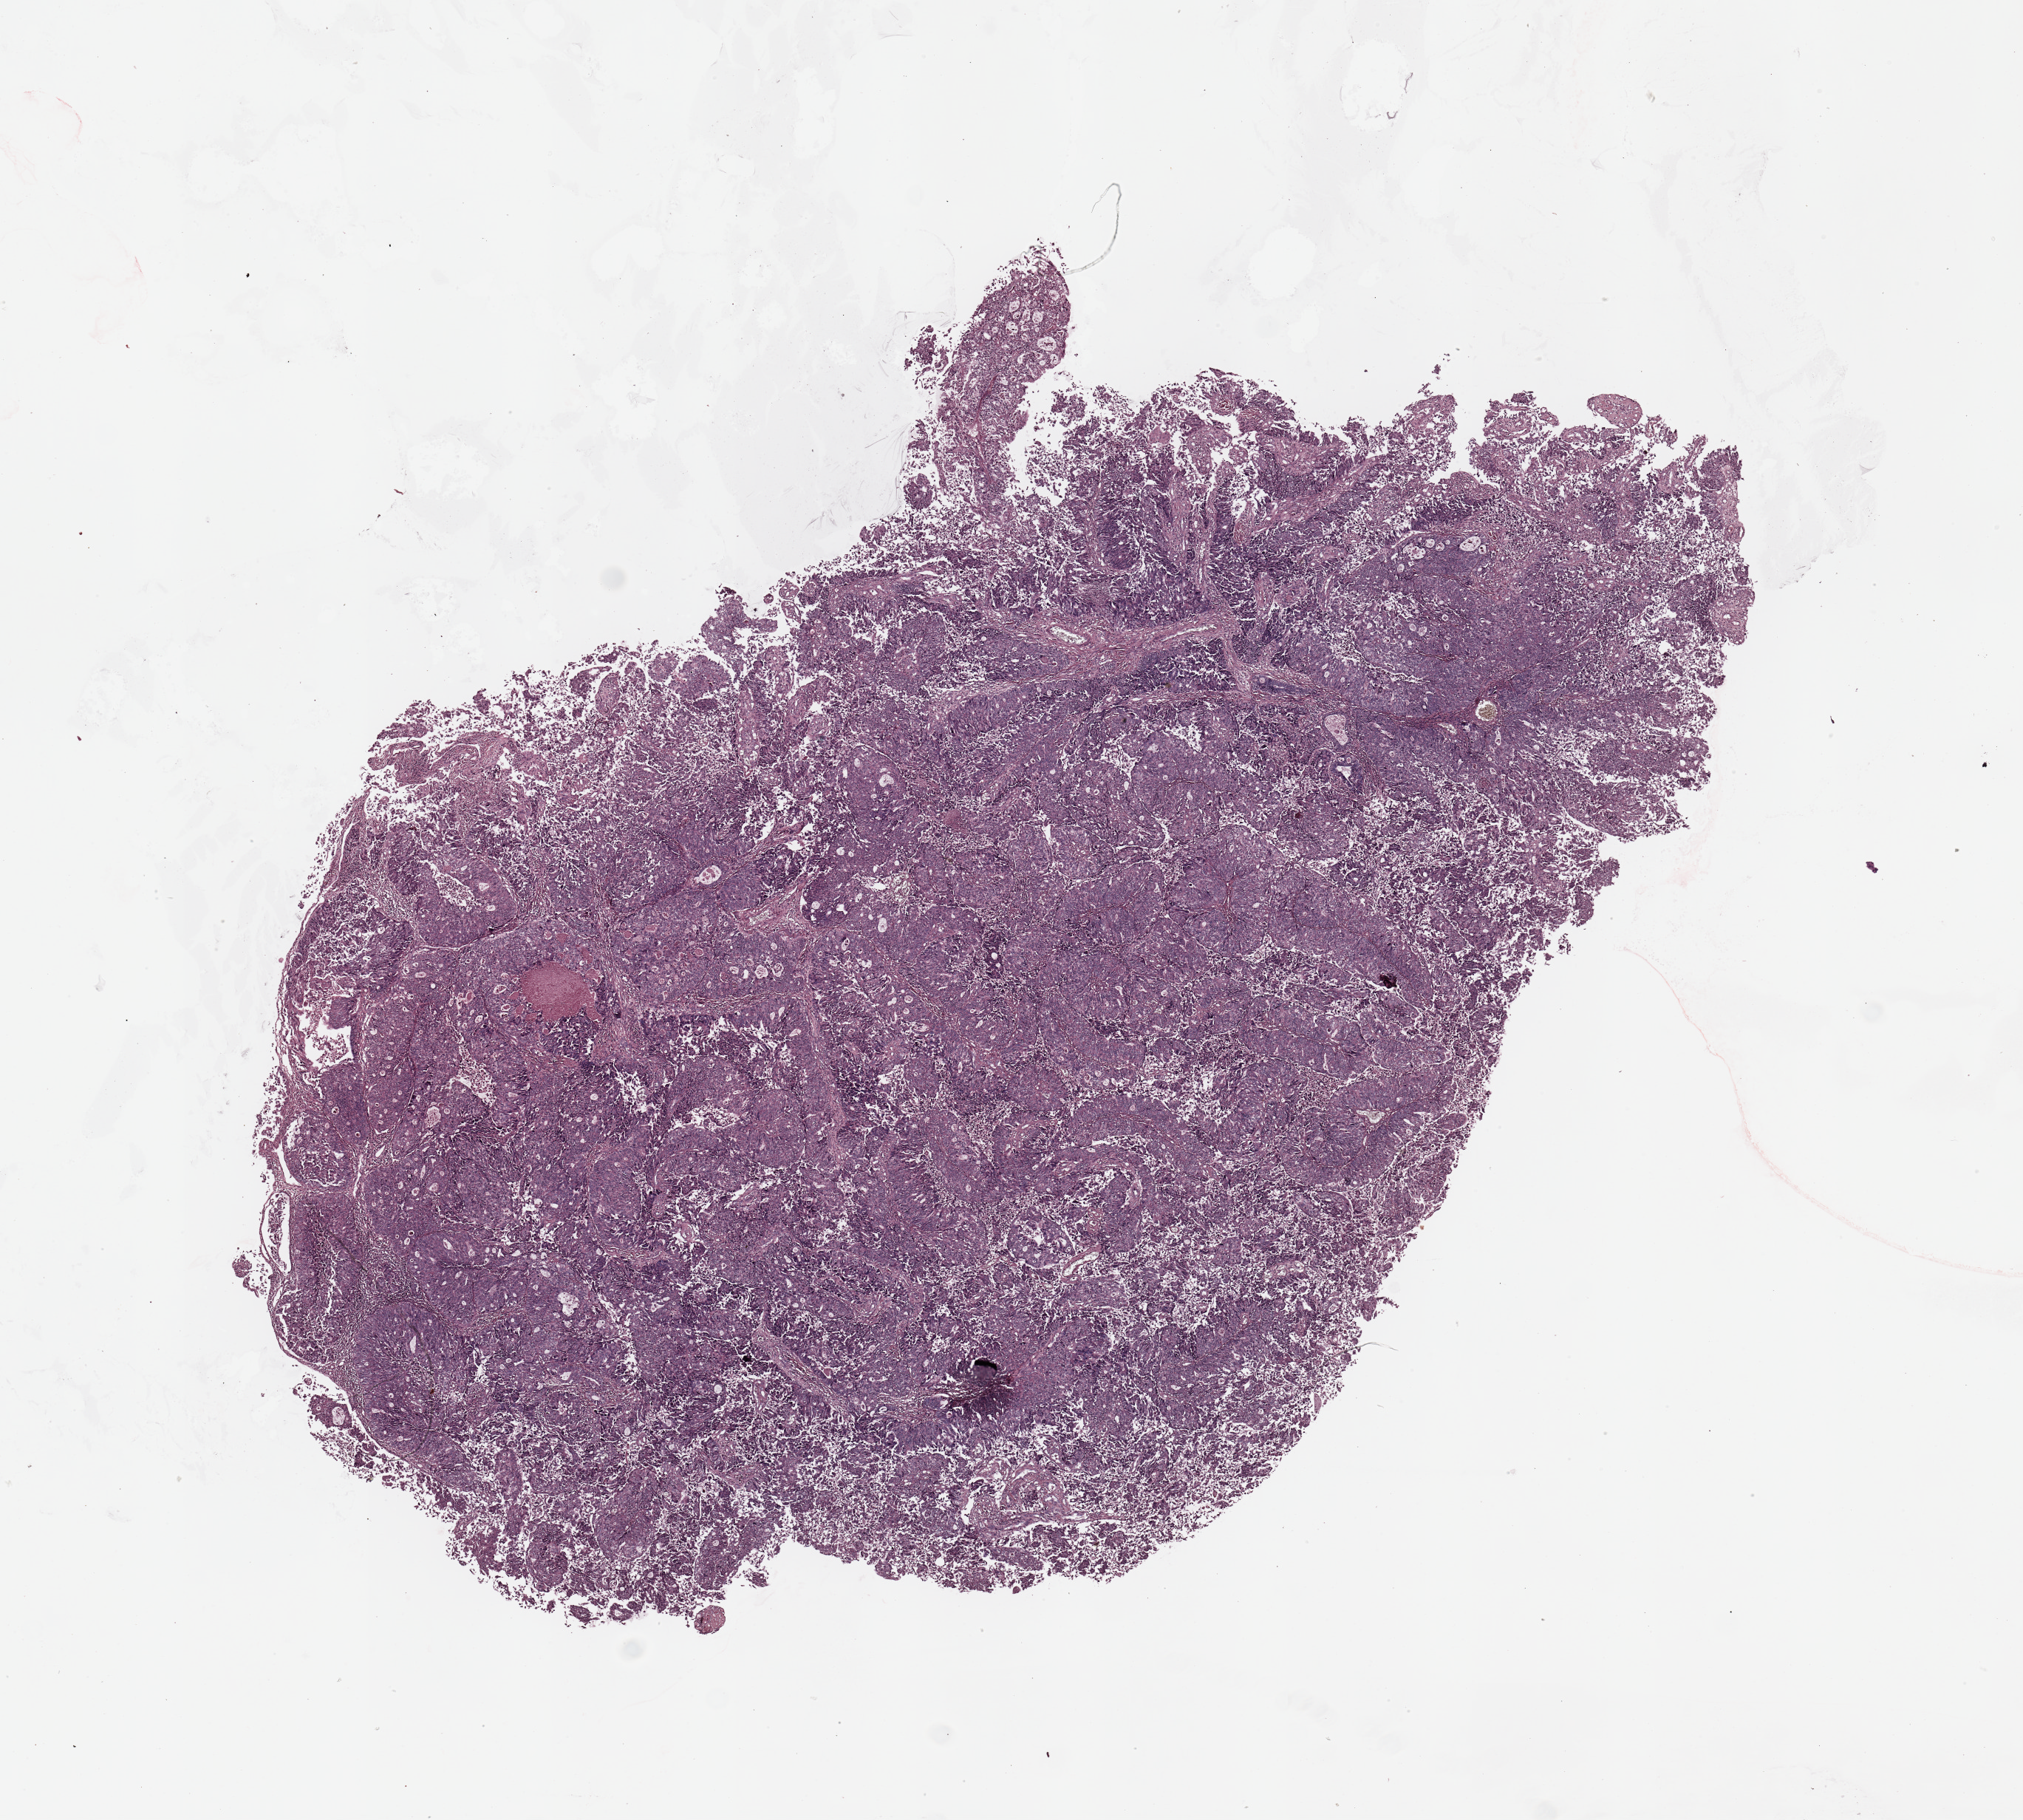
Whole-slide histology image, H&E-stained — shown as a low-resolution overview of the whole scanned area (about 10.8 x 9.7 mm, slide scanned at 20x); tumour tissue sample, uterus. Female, 75 y/o. Histologic grade: G3 (poorly differentiated).
AJCC pathologic stage: I. Diagnosis: Endometrioid adenocarcinoma, NOS.